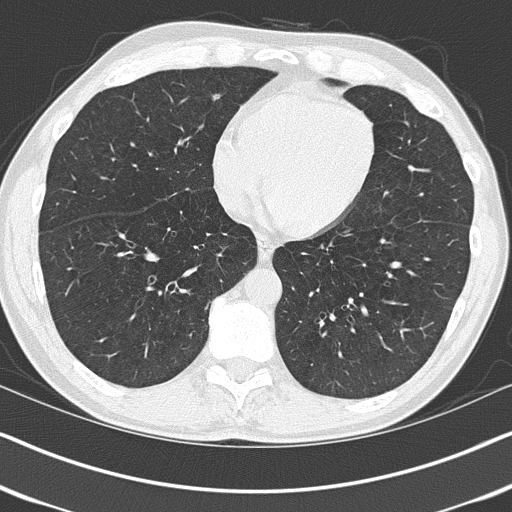
Chest CT (low-dose screening protocol), one axial image; first (baseline) screen; lung window (W 1500 / L -600 HU); slice 104 of 151 in the series. Male participant, aged 58 years at enrolment.
• Lesion marked by an expert reader, bounding box <182,78,239,119> (left, top, right, bottom; pixels).
• The exam's reader record, not a measurement of the box and not confirmed to be the same lesion: non-calcified nodule or mass ≥4 mm, right middle lobe, 5 × 5 mm, soft tissue attenuation.
• Official screen result: positive, change unspecified: nodule(s) >= 4 mm or enlarging nodule(s), mass(es), or other non-specific abnormalities suspicious for lung cancer.
• Participant outcome: lung cancer diagnosed 421 days after this screen (after the second annual screen) — adenocarcinoma, NOS, right middle lobe, moderately differentiated (G2), stage IIA (AJCC 6th edition), 10 mm at pathology.